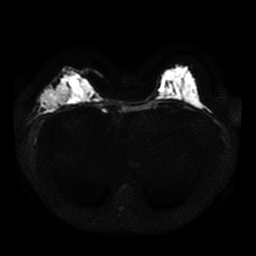
Breast MRI, one axial slice. Slice 16 of 41 in the series (ordered by position). Diffusion-weighted series; image 2 of 4 stored at this slice position (different b-values; order by instance number). 1.5 T. 5 mm slice thickness. 256 × 256 image matrix, field of view 330 × 330 mm. Female patient.
Annotated regions visible in this slice (manually delineated by an expert):
- tumour on diffusion-weighted imaging: bounding box (x1, y1, x2, y2) in pixels: (39, 85, 70, 111)